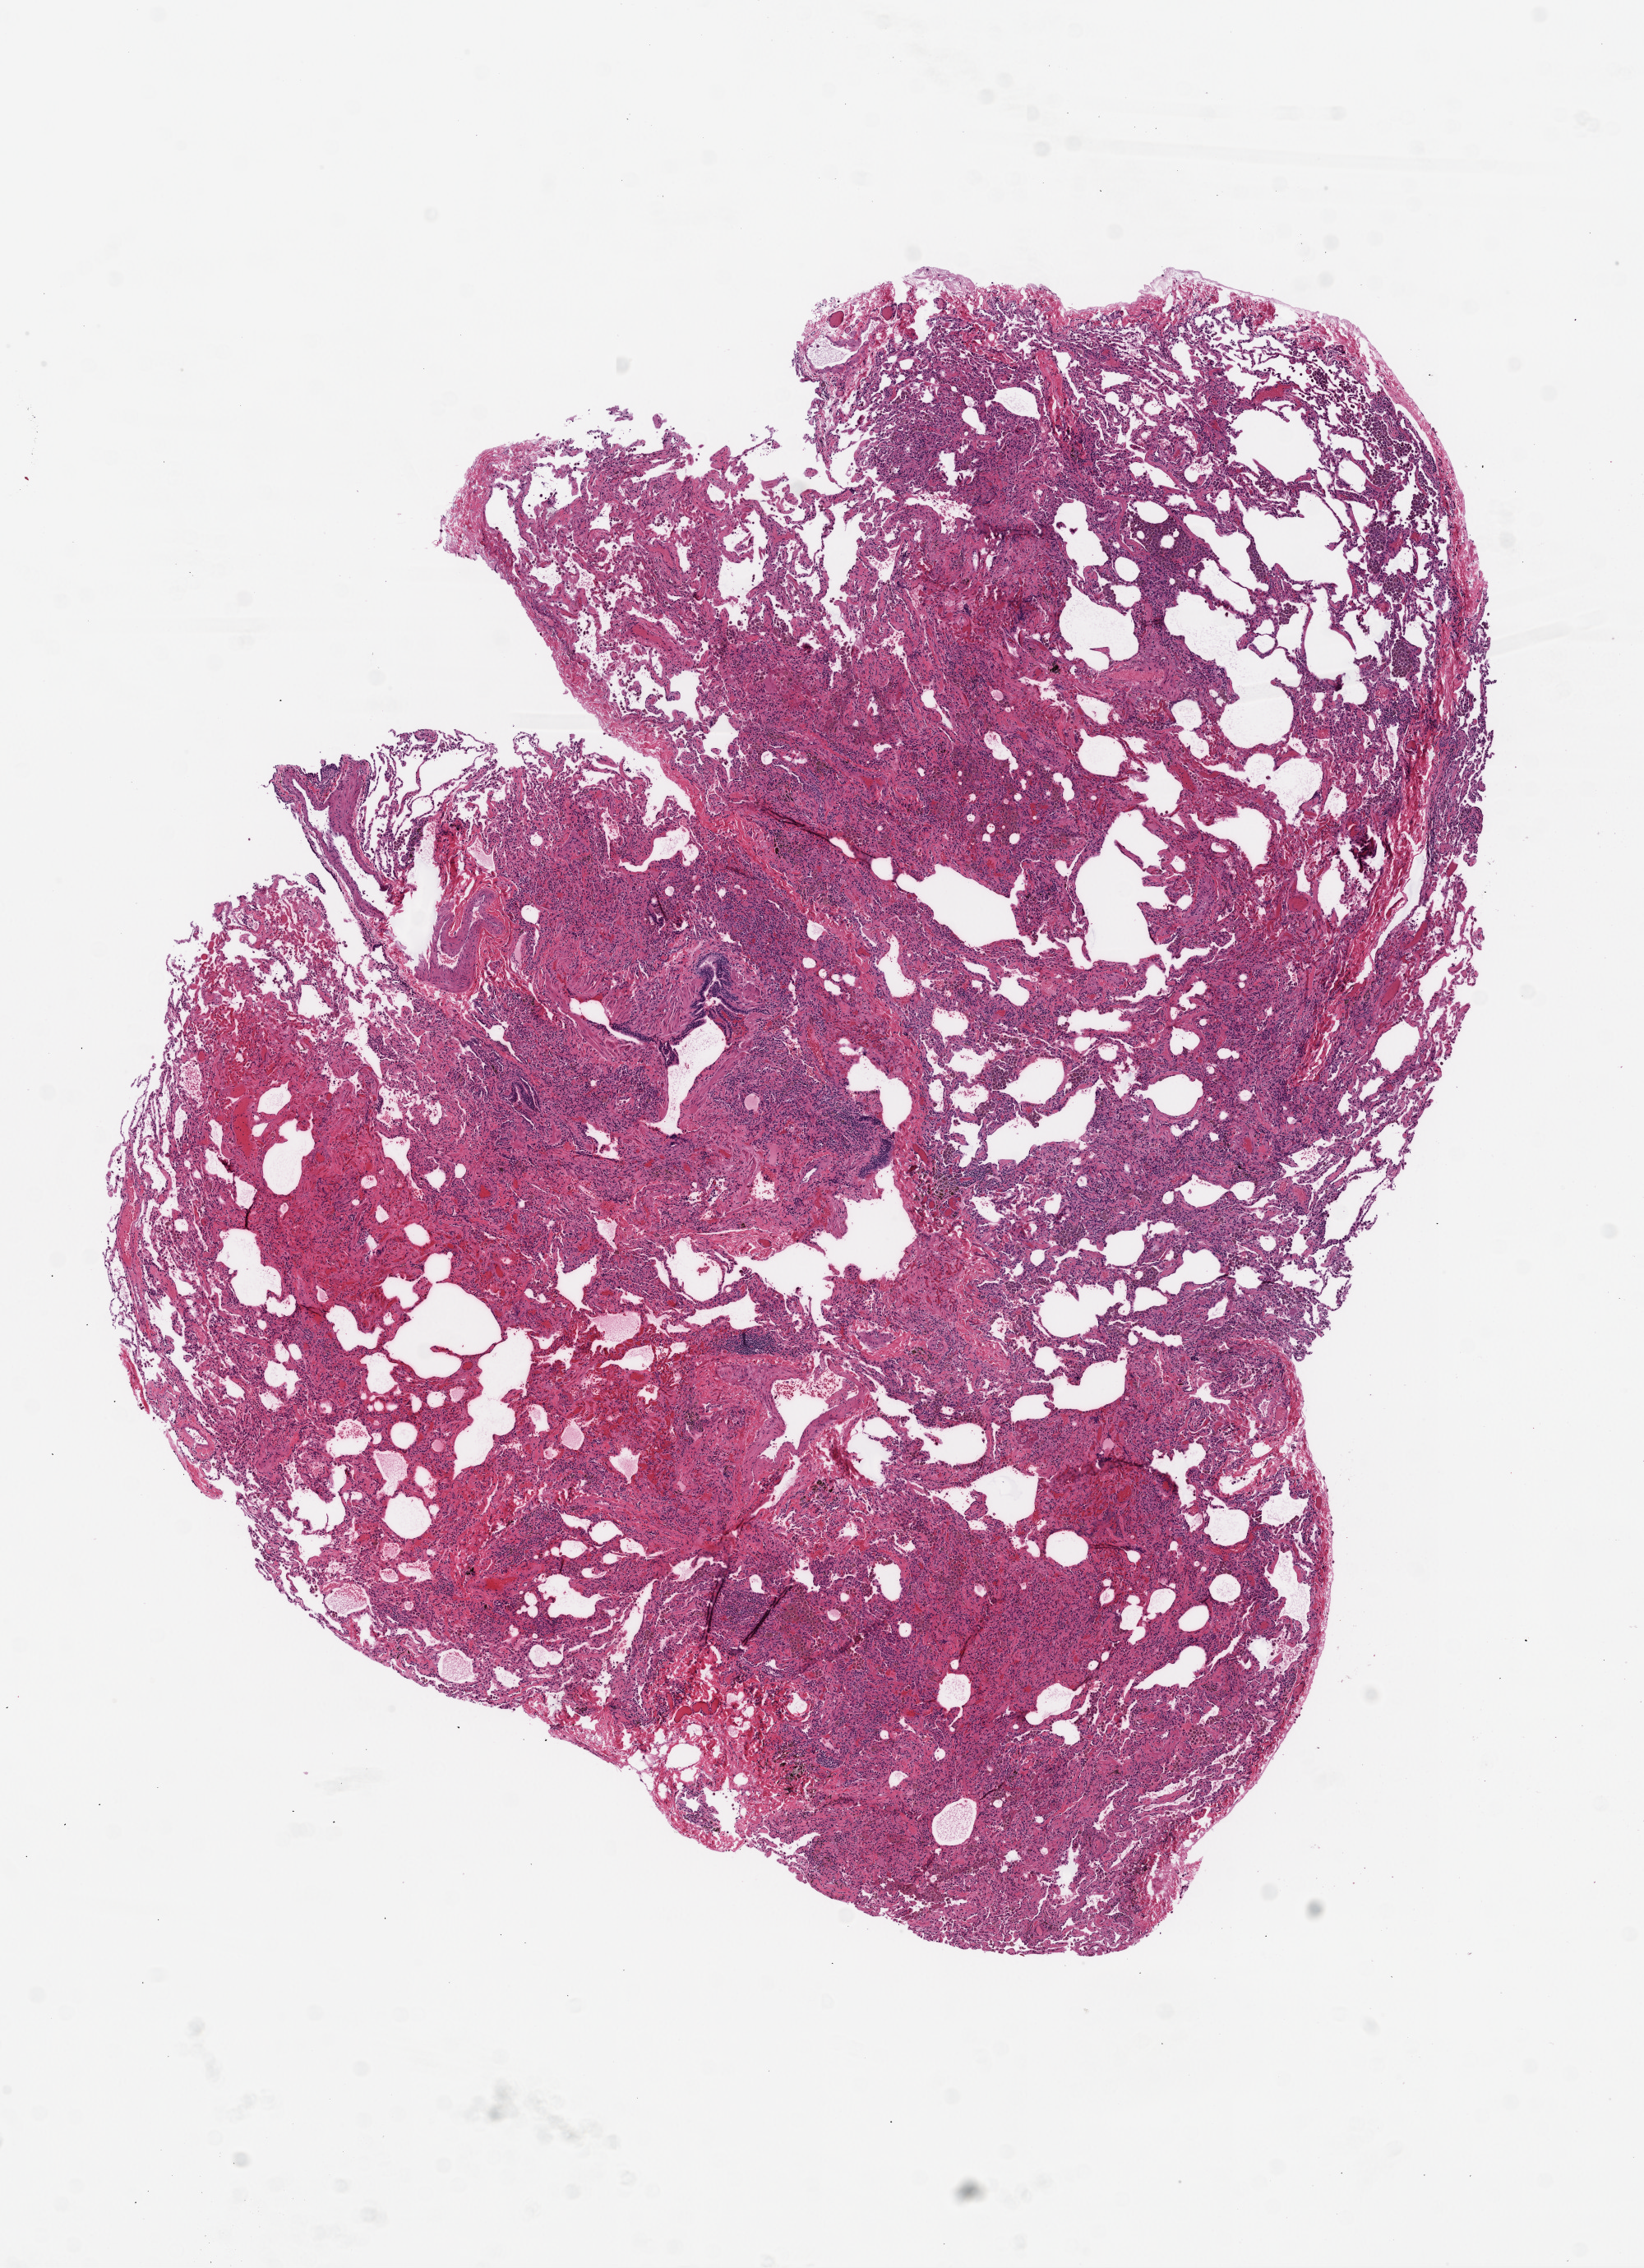
Digitized H&E-stained tissue section (whole slide), low-resolution overview of the scanned area, about 8.0 x 11.1 mm (from a 20x scan), frozen section, lung, solid tissue normal (non-tumour tissue) sample. Patient: female, age at initial diagnosis 33 years.
This section: solid tissue normal sample (biorepository sample class). Patient diagnosis: Adenocarcinoma, NOS (upper lobe, lung).